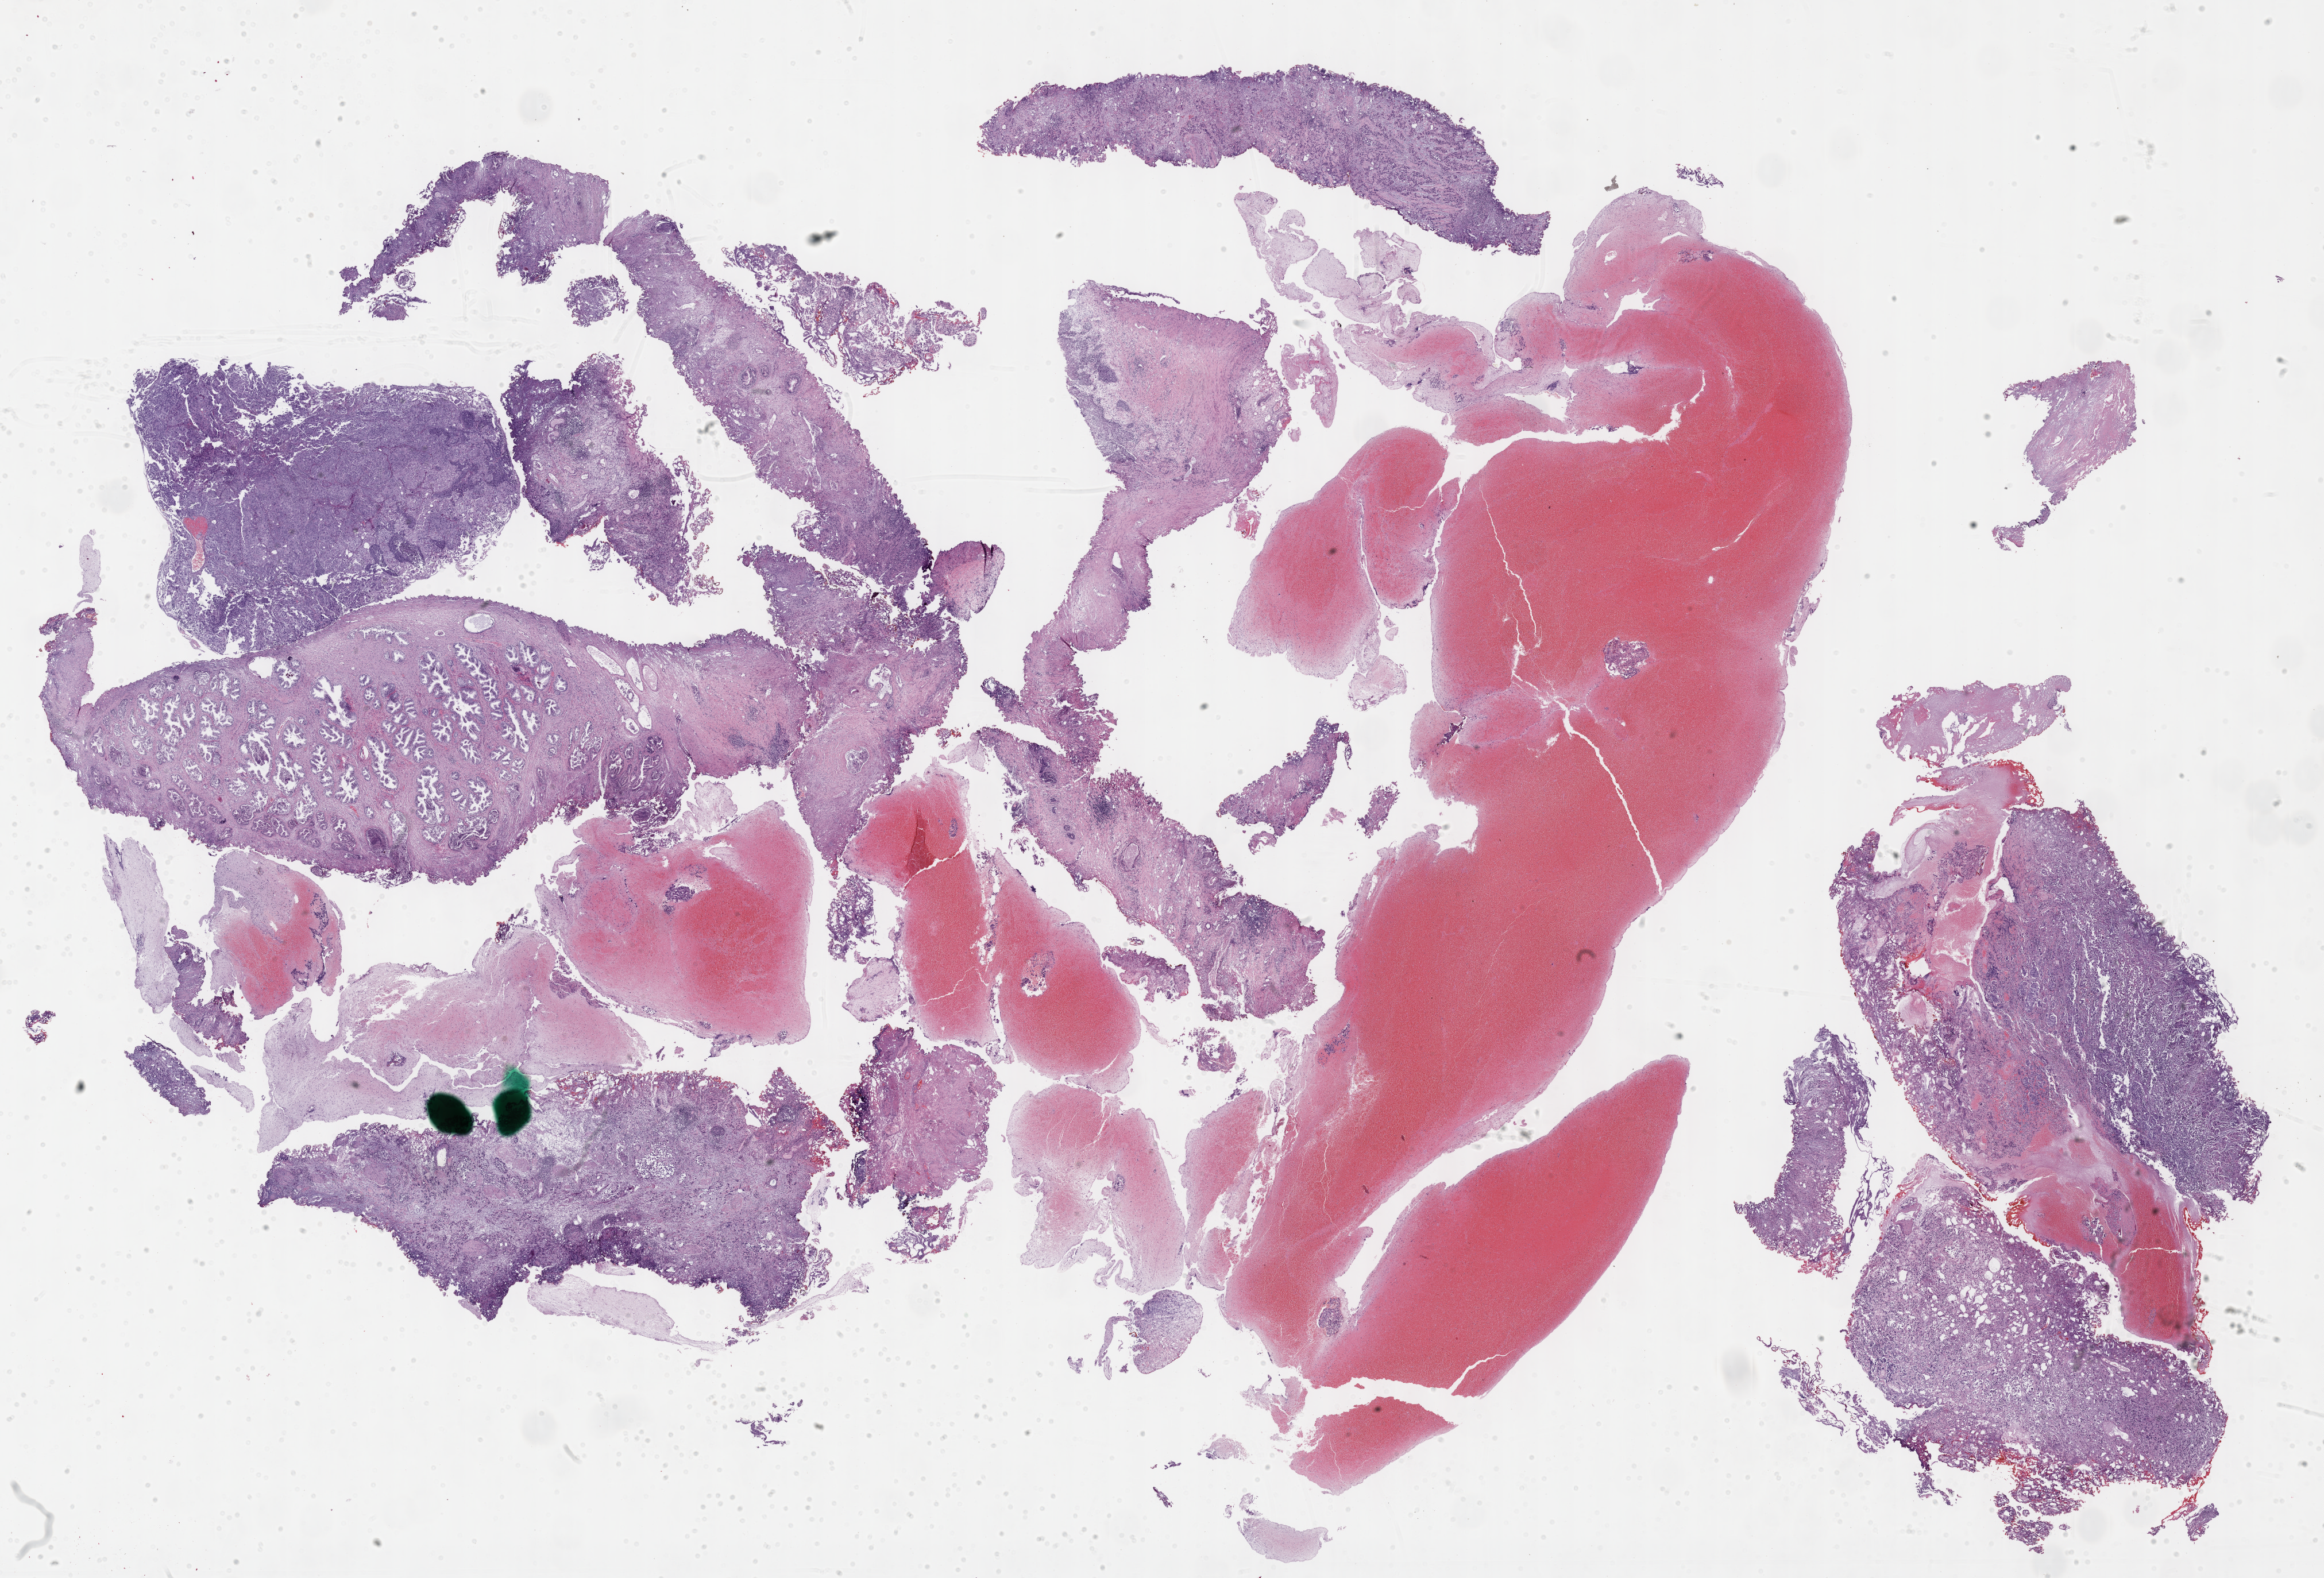
H&E whole-slide image — whole scanned area (about 32.7 x 22.2 mm) shown as a low-resolution overview; FFPE section; sample: primary tumour, bladder. Patient: male, age at initial diagnosis 77 years. Histologic grade: high grade.
* pathologic diagnosis: Transitional cell carcinoma
* AJCC pathologic stage: IV